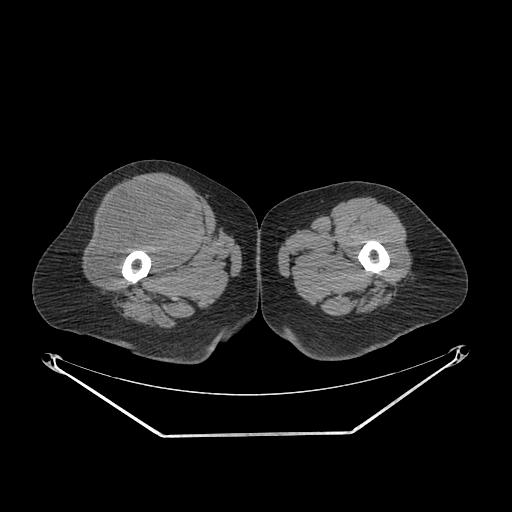
CT of an extremity soft-tissue mass (from a PET/CT study), one axial slice. Reconstruction kernel SOFT. 140 kVp. Soft-tissue window (W 400 / L 40 HU). 512 × 512 image matrix, field of view 500 × 500 mm. Female patient. Case-level facts recorded for this patient, not image findings: histological type: pleiomorphic undifferentiated sarcoma; grade: high; site of the primary tumour: right quadricep.
Structures marked on this image (expert contour drawn on MRI and transferred to this co-registered scan by the dataset authors):
- tumour plus oedema (research contour): bounding box <91,183,197,284> (left, top, right, bottom; pixels)
- tumour (research contour): <91,183,197,284>